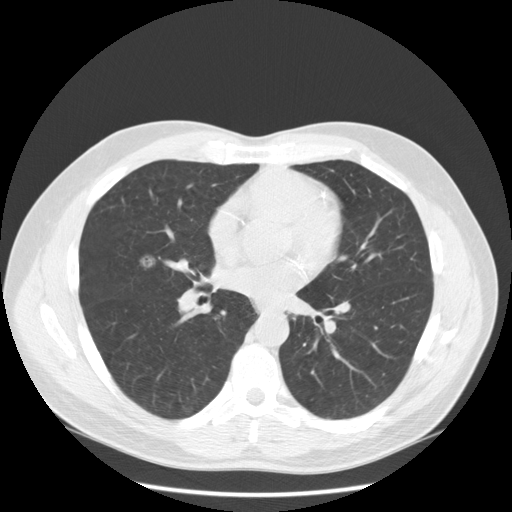
Low-dose screening chest CT, one axial slice; slice 108 of 234 in the series (ordered by position); reconstruction kernel STANDARD; lung window (W 1500 / L -600 HU); 512 × 512 image matrix, field of view 385 × 385 mm.
Outlined on this slice (expert manual segmentation):
- lesion 1 (tumor, middle lobe of right lung): bounding box [x1, y1, x2, y2] px = [140, 255, 156, 268]